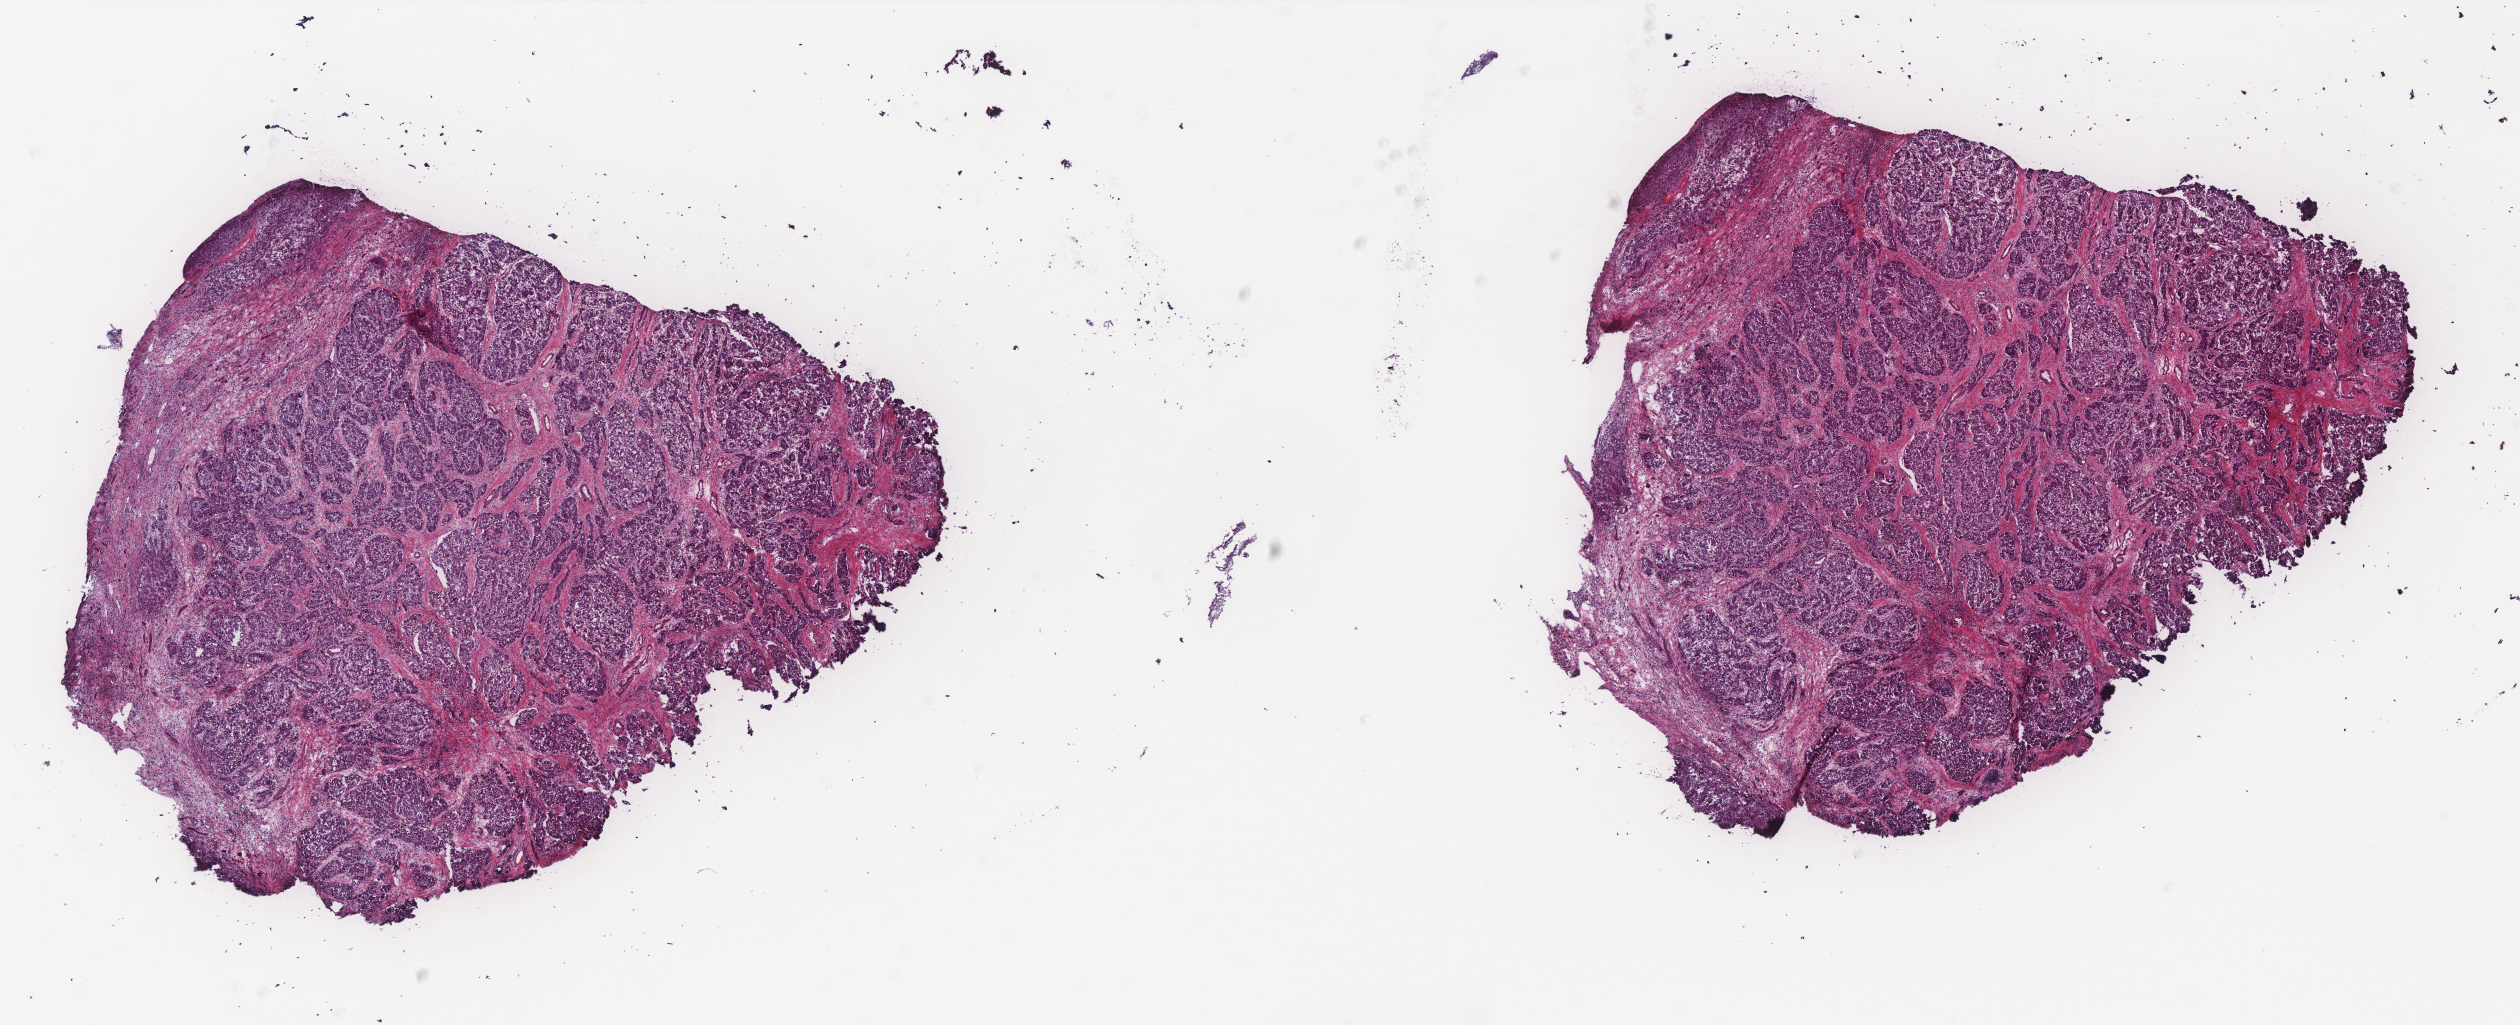
Digitized H&E tissue section (whole slide), shown as a low-resolution overview of the whole scanned area (about 20.2 x 8.2 mm, slide scanned at 40x); frozen section; primary tumour sample from the liver. Patient: male, age at initial diagnosis 46 years. Histologic grade: G2 (moderately differentiated). Pathologist review of this section (percent, as recorded): tumour cells 70%, tumour nuclei 70%, normal cells 0%, stromal cells 30%, necrosis 0%. Infiltration values recorded for this section: lymphocyte infiltration 5%, monocyte infiltration 0%, neutrophil infiltration 0%.
AJCC pathologic stage: I (6th edition). TNM: T1 N0 M0. Histologic diagnosis: Hepatocellular carcinoma, NOS.